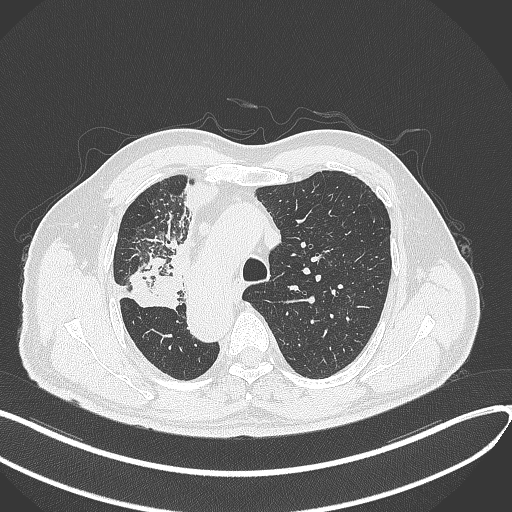
Chest CT, one axial slice. Position 231 of 300 along the scan axis. Reconstruction kernel B70f. Lung window (W 1500 / L -600 HU). 1 mm slice thickness. 512 × 512 image matrix, field of view 400 × 400 mm. Male patient, age 67 years. Case-level facts recorded for this patient, not image findings: clinical TNM (as recorded): T2a N0 M0.
Structures marked on this image (rectangle marked by the reading radiologist):
- lung tumour (recorded histology: squamous cell carcinoma): box from (x=130, y=252) to (x=183, y=313) px